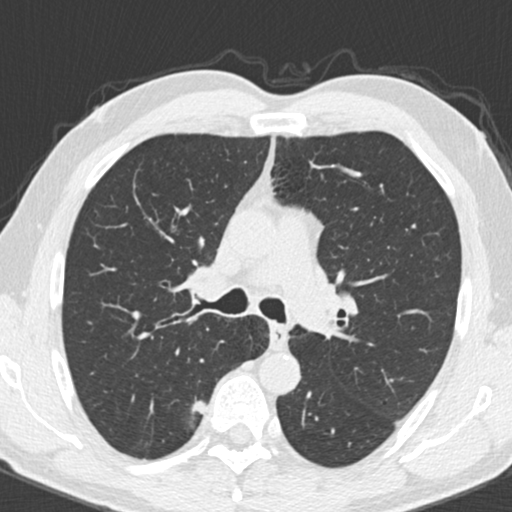
Chest CT (low-dose screening protocol), one axial image. Third screening round (two years after baseline). Lung window (W 1500 / L -600 HU). 2 mm slice thickness. 120 kVp. Male, age 55 years at enrolment. Current smoker at enrolment.
• Expert reader's lesion annotation, box from (x=170, y=389) to (x=220, y=438) px.
• Reader record for this screening exam (exam-level; its link to the box is not recorded): non-calcified nodule or mass ≥4 mm, right upper lobe, 9 × 7 mm, smooth margins, soft tissue attenuation, pre-existing on the prior screen: no.
• Participant outcome: lung cancer diagnosed 221 days after this screen — adenocarcinoma, NOS, right upper lobe, poorly differentiated (G3), stage IA (AJCC 6th edition), 15 mm at pathology.